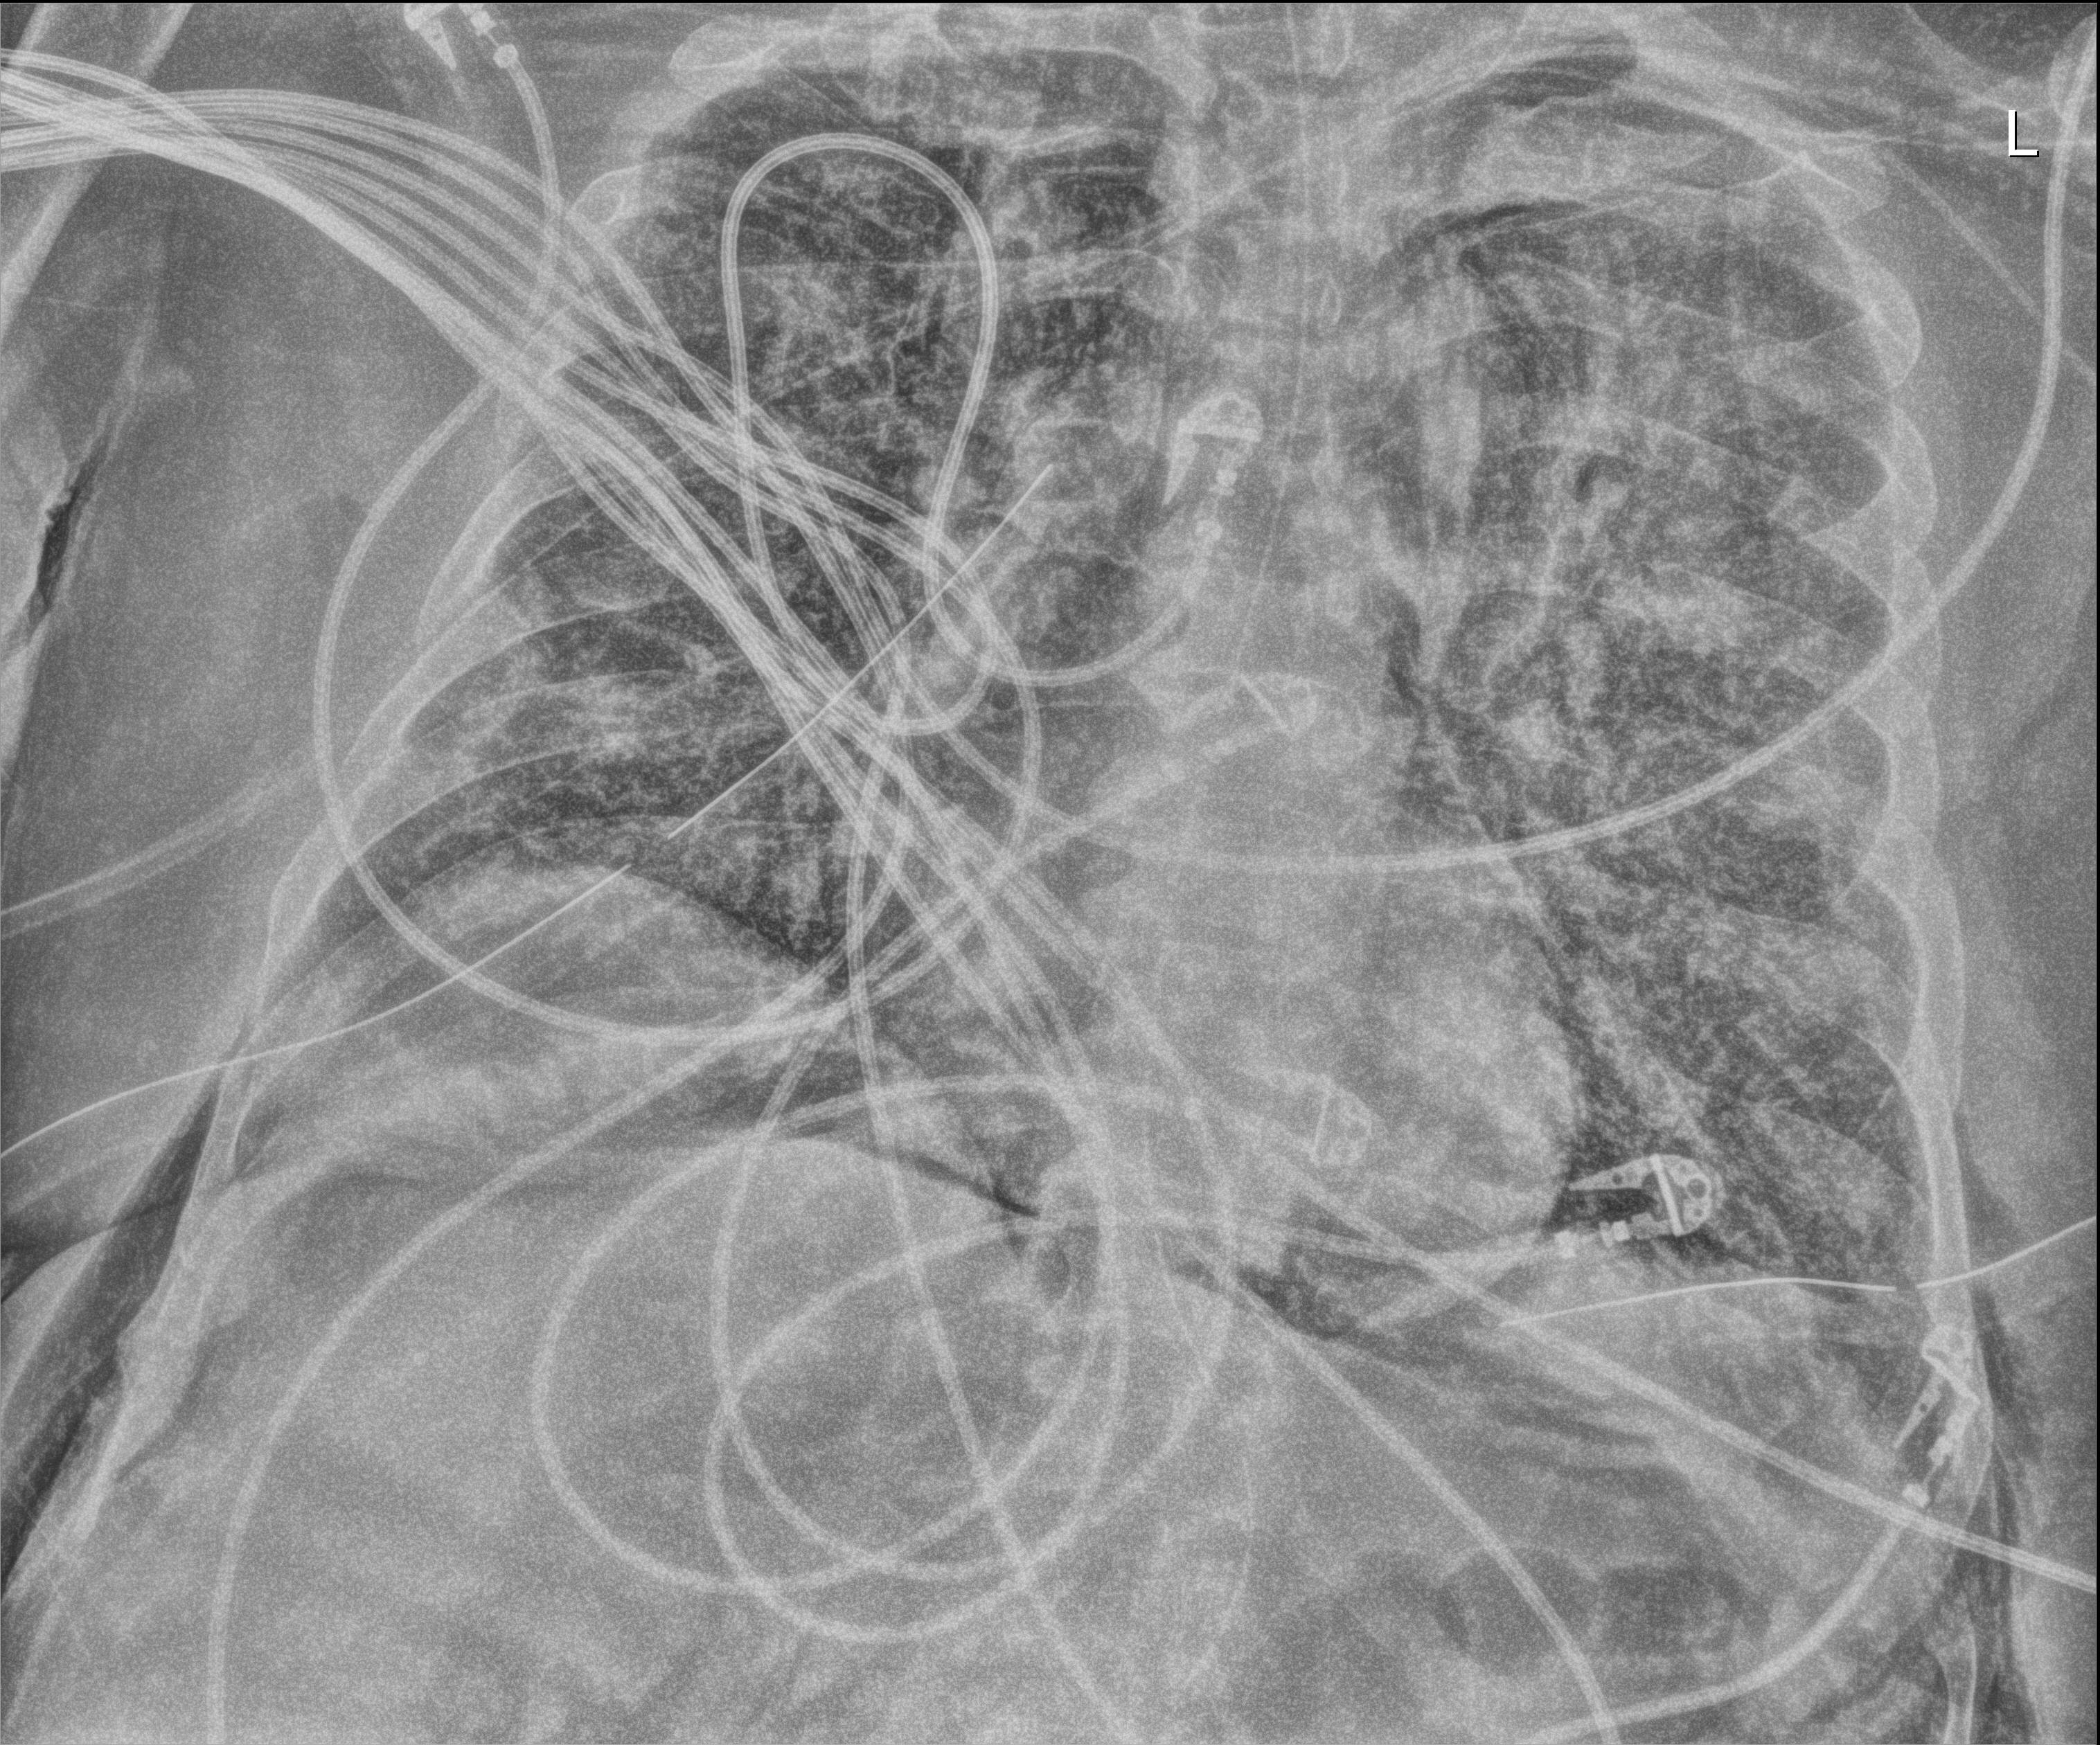
Portable chest radiograph, anteroposterior (AP) projection. Adult patient hospitalised with COVID-19, age 18–59 years.
Admission-level facts for this patient (not findings on this image; timing relative to this image not recorded):
- admitted to intensive care during this hospital stay: yes
- mechanically ventilated during this hospital stay: yes
- length of hospital stay: 28 days